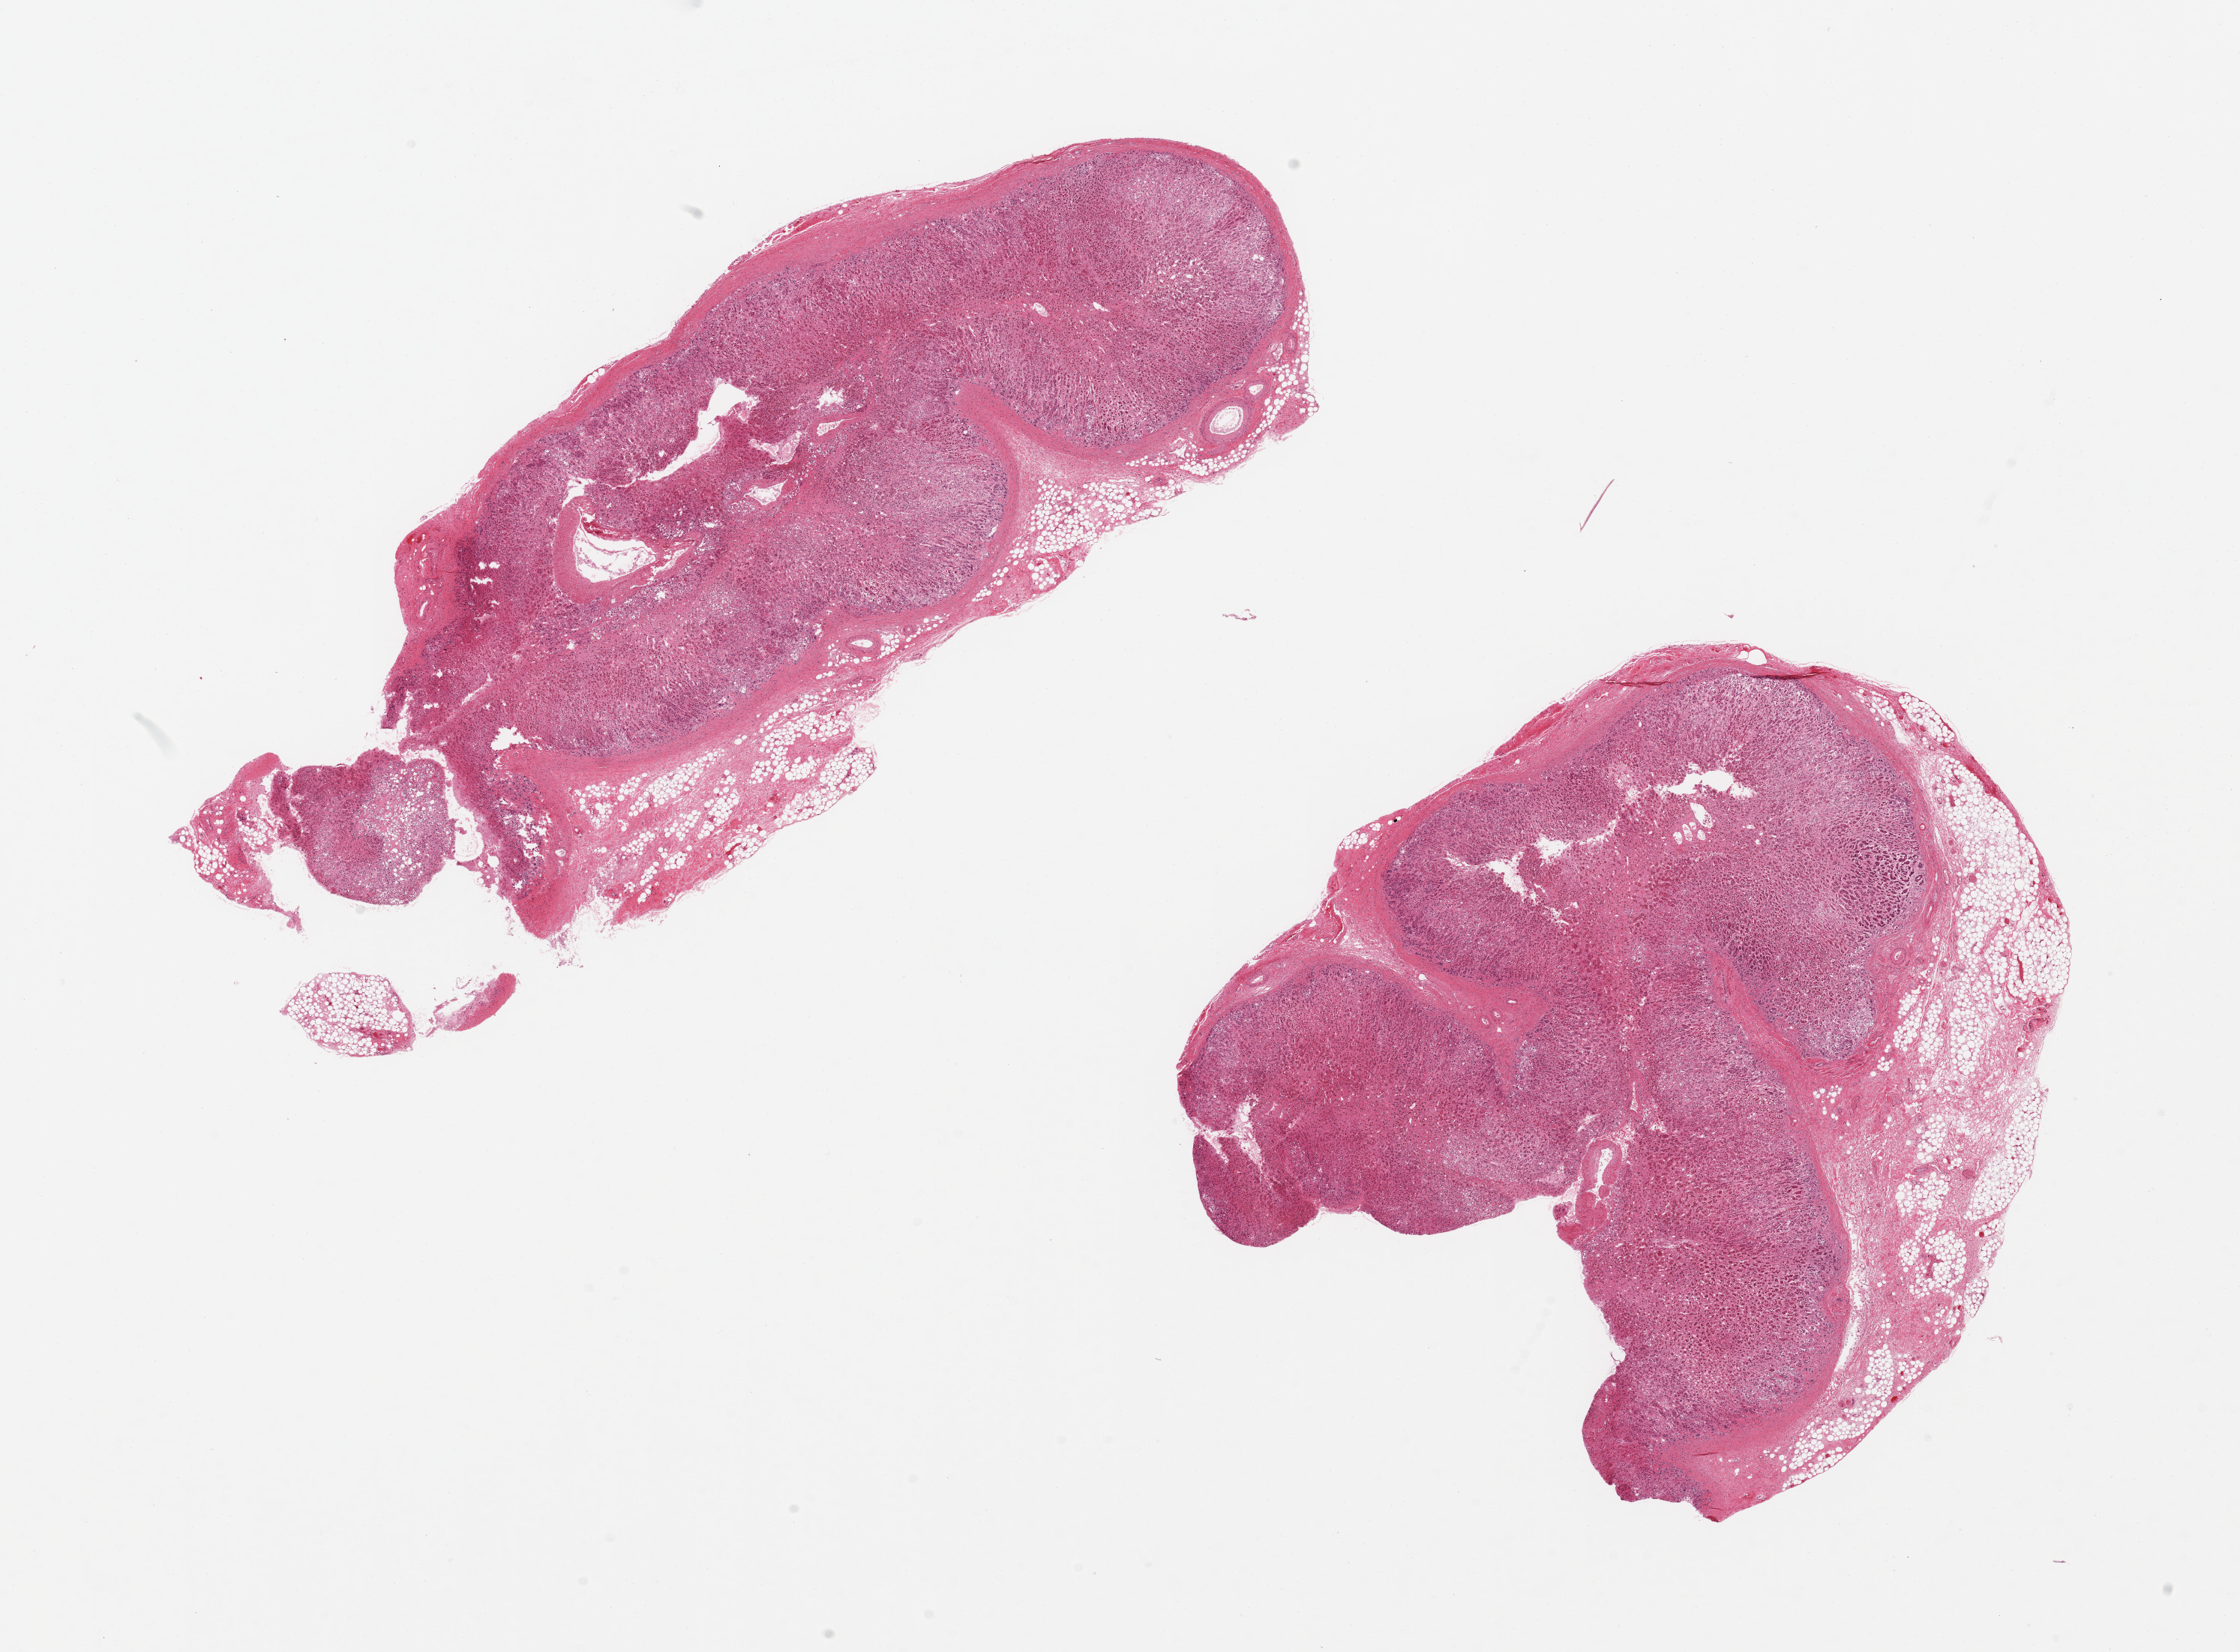
Whole-slide image, H&E stain, shown as a low-resolution overview of the whole scanned area (about 23.6 x 17.4 mm); PAXgene-fixed, paraffin-embedded tissue; target tissue: adrenal gland; donor tissue sample.
• pathologist's review note for this sample: 3 pieces 10x5 & 9x8 mm; ~20% adjacent adipose